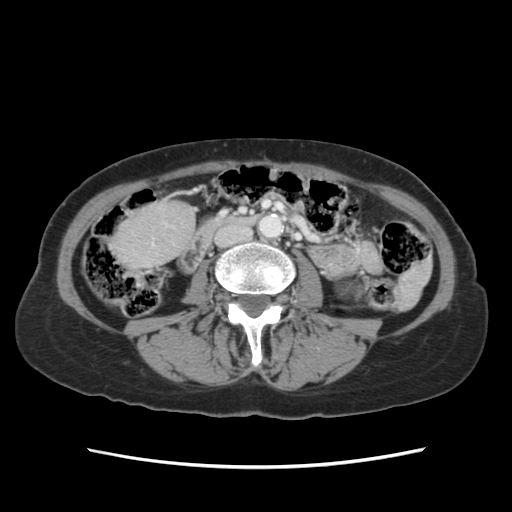
Contrast-enhanced abdominal CT, one axial slice; slice 17 of 120 in the series (ordered by position); 120 kVp; intravenous contrast given; soft-tissue window (W 400 / L 40 HU); 512 × 512 image matrix. Female patient, age 70 years. From the clinical record (not read from this slice): diagnosis: colorectal cancer liver metastases, imaged before liver resection; multiple liver metastases: no; largest metastasis: 2.5 cm; chemotherapy before resection: yes.
Annotated regions visible in this slice (outlined manually by an expert reader):
- liver: bounding box (x1, y1, x2, y2) in pixels: (115, 203, 191, 266)
- planned liver remnant (the part of the liver to remain after resection): (116, 204, 191, 266)